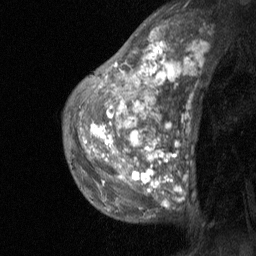
Breast MRI (dynamic contrast-enhanced), one sagittal slice; position 42 of 64 along the scan axis; dynamic contrast-enhanced study with each time point stored as its own series, time point 2 of 3 at this slice position (early post-contrast, ordered by acquisition time); 1.5 T; TE 4.8 ms, TR 27 ms; 2 mm slice thickness; 256 × 256 image matrix, field of view 180 × 180 mm. Female patient, age 36 years. Case-level facts recorded for this patient, not image findings: setting: breast cancer imaged before/during neoadjuvant chemotherapy; receptor status: HR-positive, HER2-negative.
Structures marked on this image (semi-automatic segmentation, software-assisted and operator-edited):
- analysis volume of interest (the breast-tissue region the enhancement analysis was run in; not a lesion): bounding box [x1, y1, x2, y2] px = [67, 12, 200, 223]
- tumour enhancement mask (voxels above the 90 % enhancement threshold inside the analysis volume of interest): [91, 29, 174, 204]